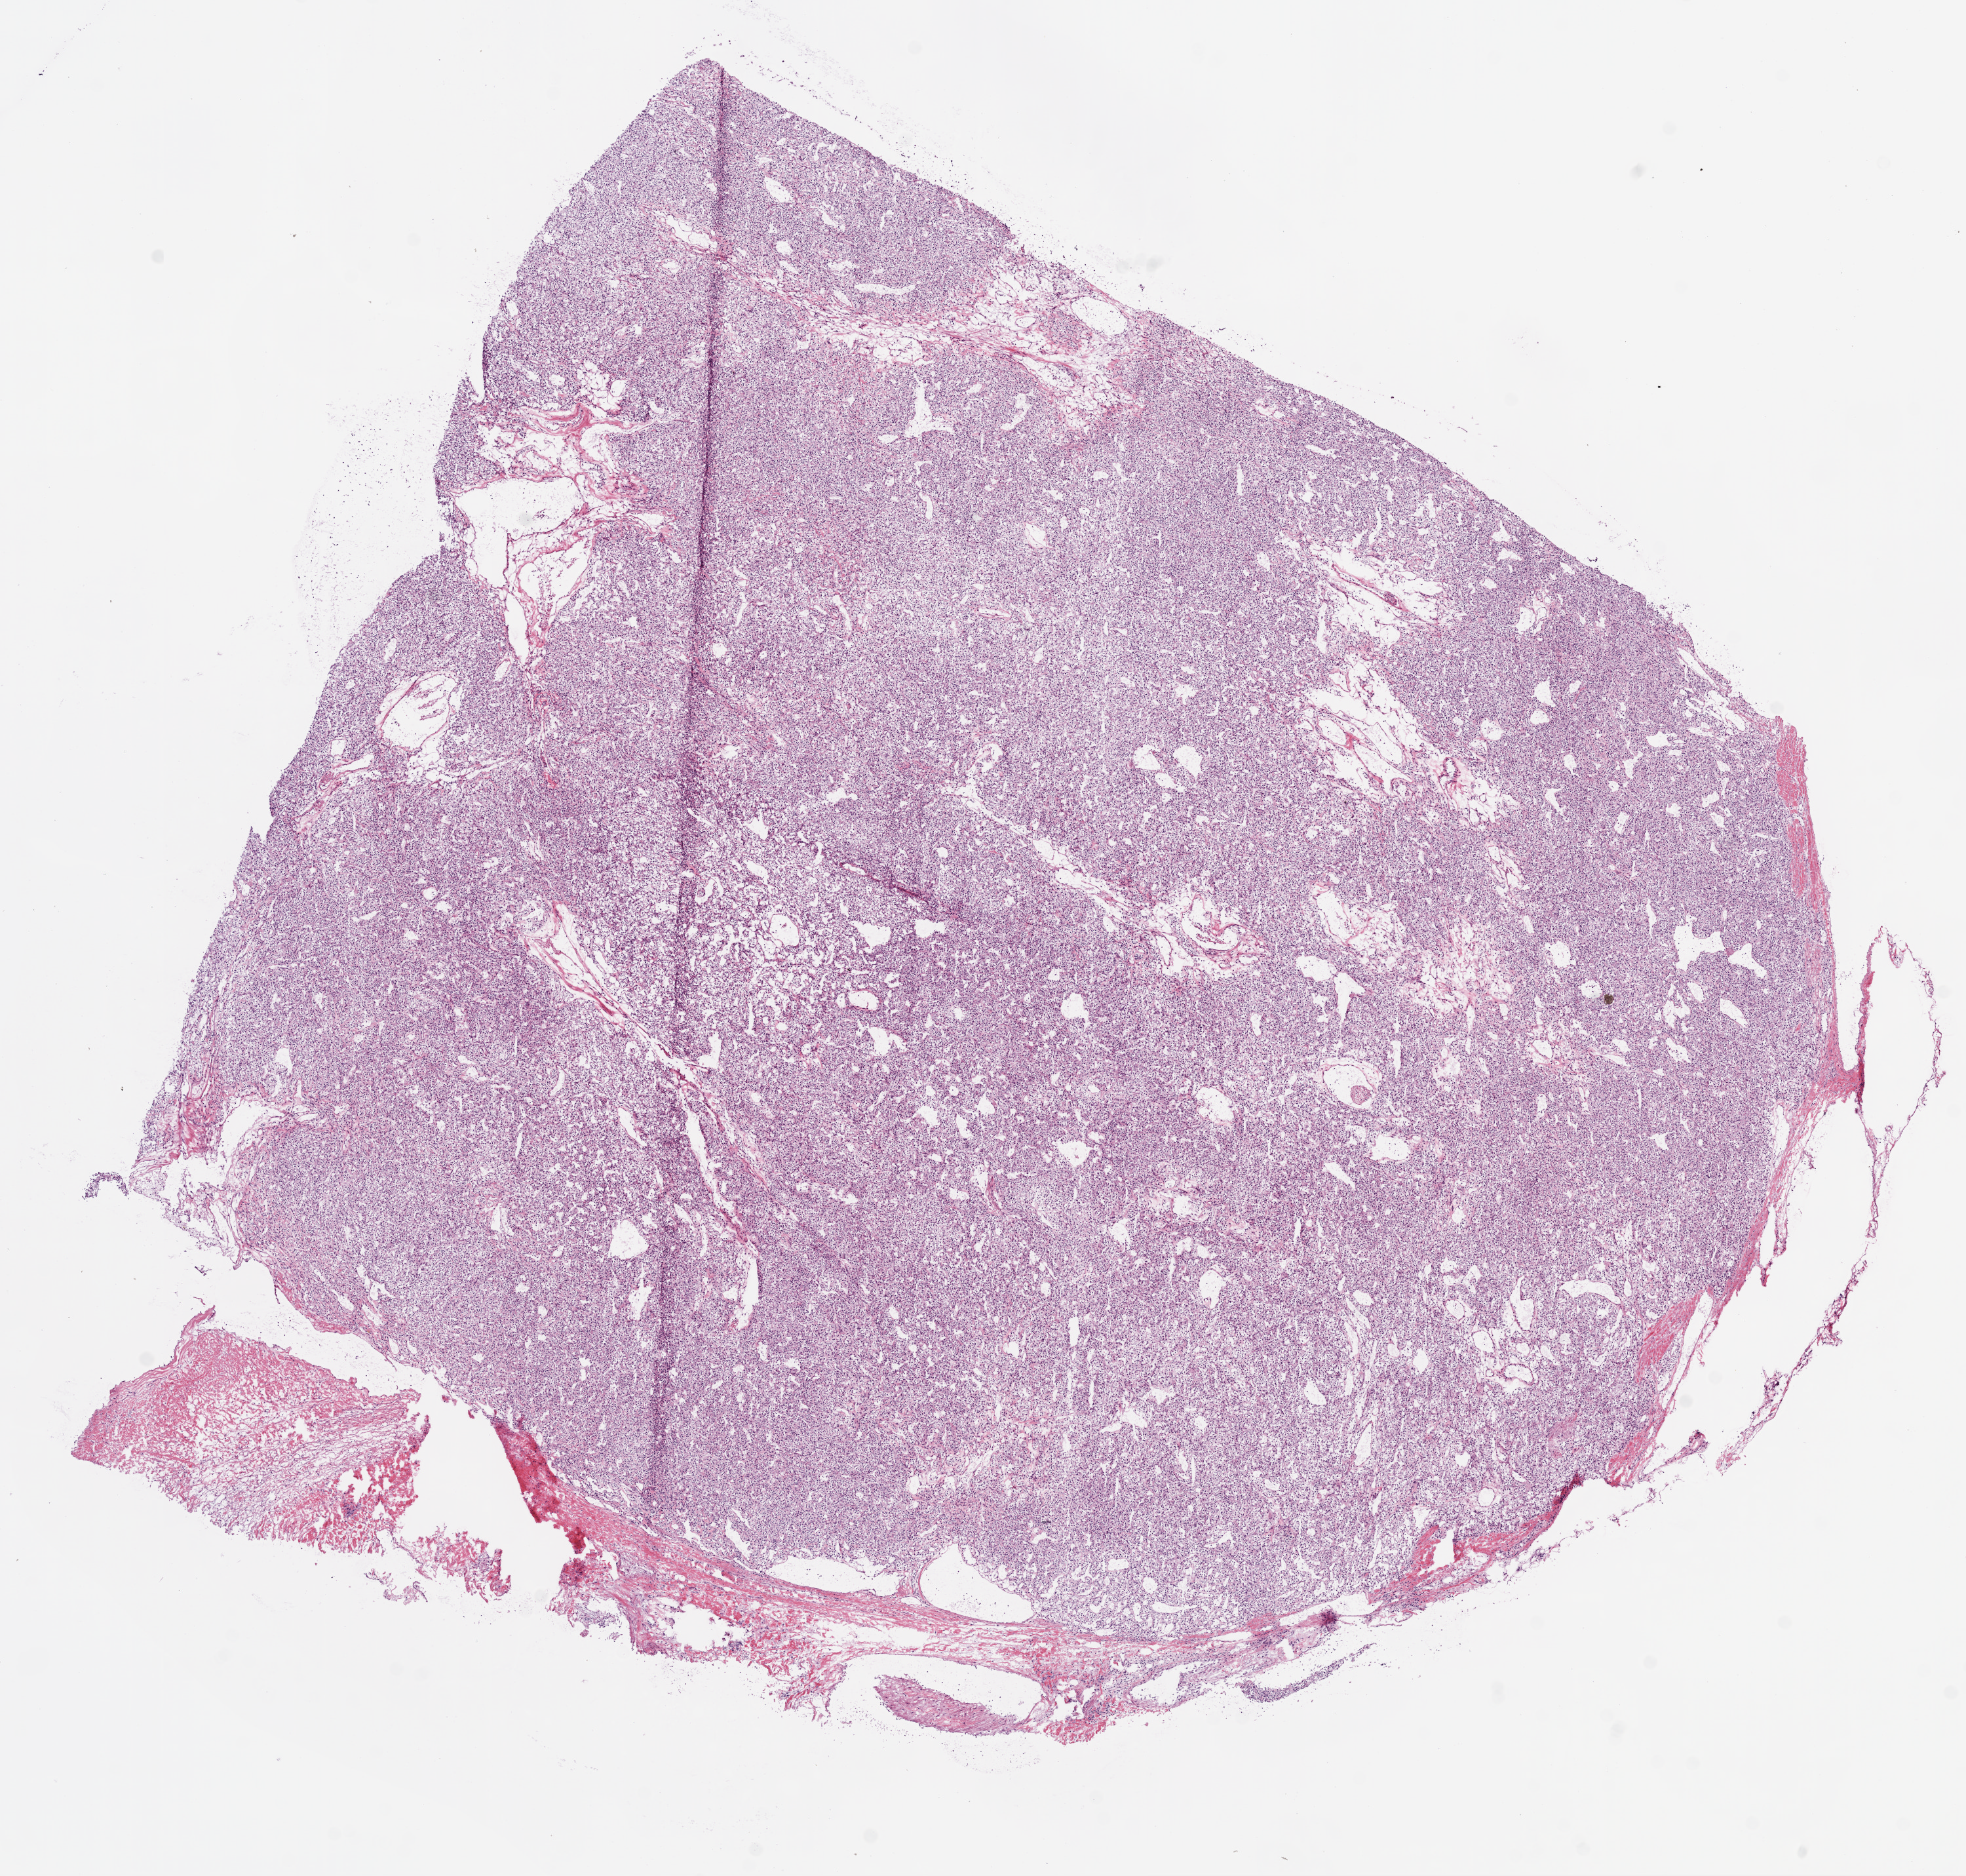
Whole-slide histology image, H&E, shown as a low-resolution overview of the whole scanned area (about 12.0 x 11.5 mm, acquisition: 20x scan). Frozen section from the bottom of the tissue portion. Primary tumour sample from the kidney. Male patient; age at initial diagnosis 51 years. Histologic grade: G3 (poorly differentiated). Composition of this section per pathologist review: tumour cells 85%, tumour nuclei 90%, normal cells 0%, stromal cells 15%, necrosis 0%.
* histologic diagnosis: Clear cell adenocarcinoma, NOS
* TNM: T3a NX M0
* AJCC pathologic stage: III